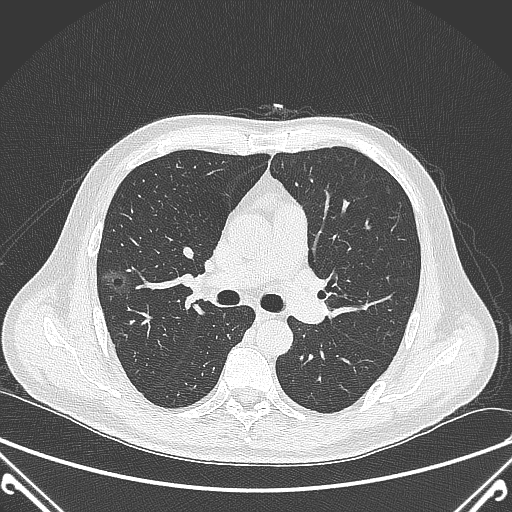
Chest CT, one axial slice. Slice 225 of 360 in the series (ordered by position). 120 kVp. Lung window (W 1500 / L -600 HU). 1 mm slice thickness. 512 × 512 image matrix. Male patient, age 64 years. From the clinical record (not read from this slice): clinical TNM (as recorded): T1c N0 M0.
Outlined on this slice (bounding box drawn by a radiologist):
- lung tumour (recorded histology: adenocarcinoma): box from (x=97, y=262) to (x=136, y=303) px